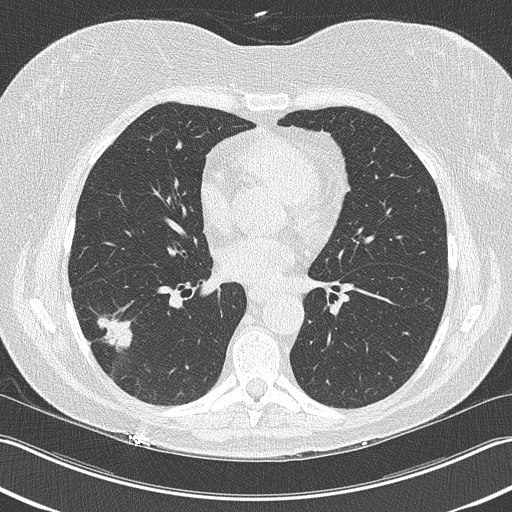
Low-dose screening chest CT, one axial slice. Position 111 of 210 along the scan axis. Reconstruction kernel B50f. 120 kVp. Lung window (W 1500 / L -600 HU). 512 × 512 image matrix.
Structures marked on this image (manually delineated by an expert):
- lesion 1 (tumor, lower lobe of right lung): bounding box (x1, y1, x2, y2) in pixels: (97, 315, 135, 352)